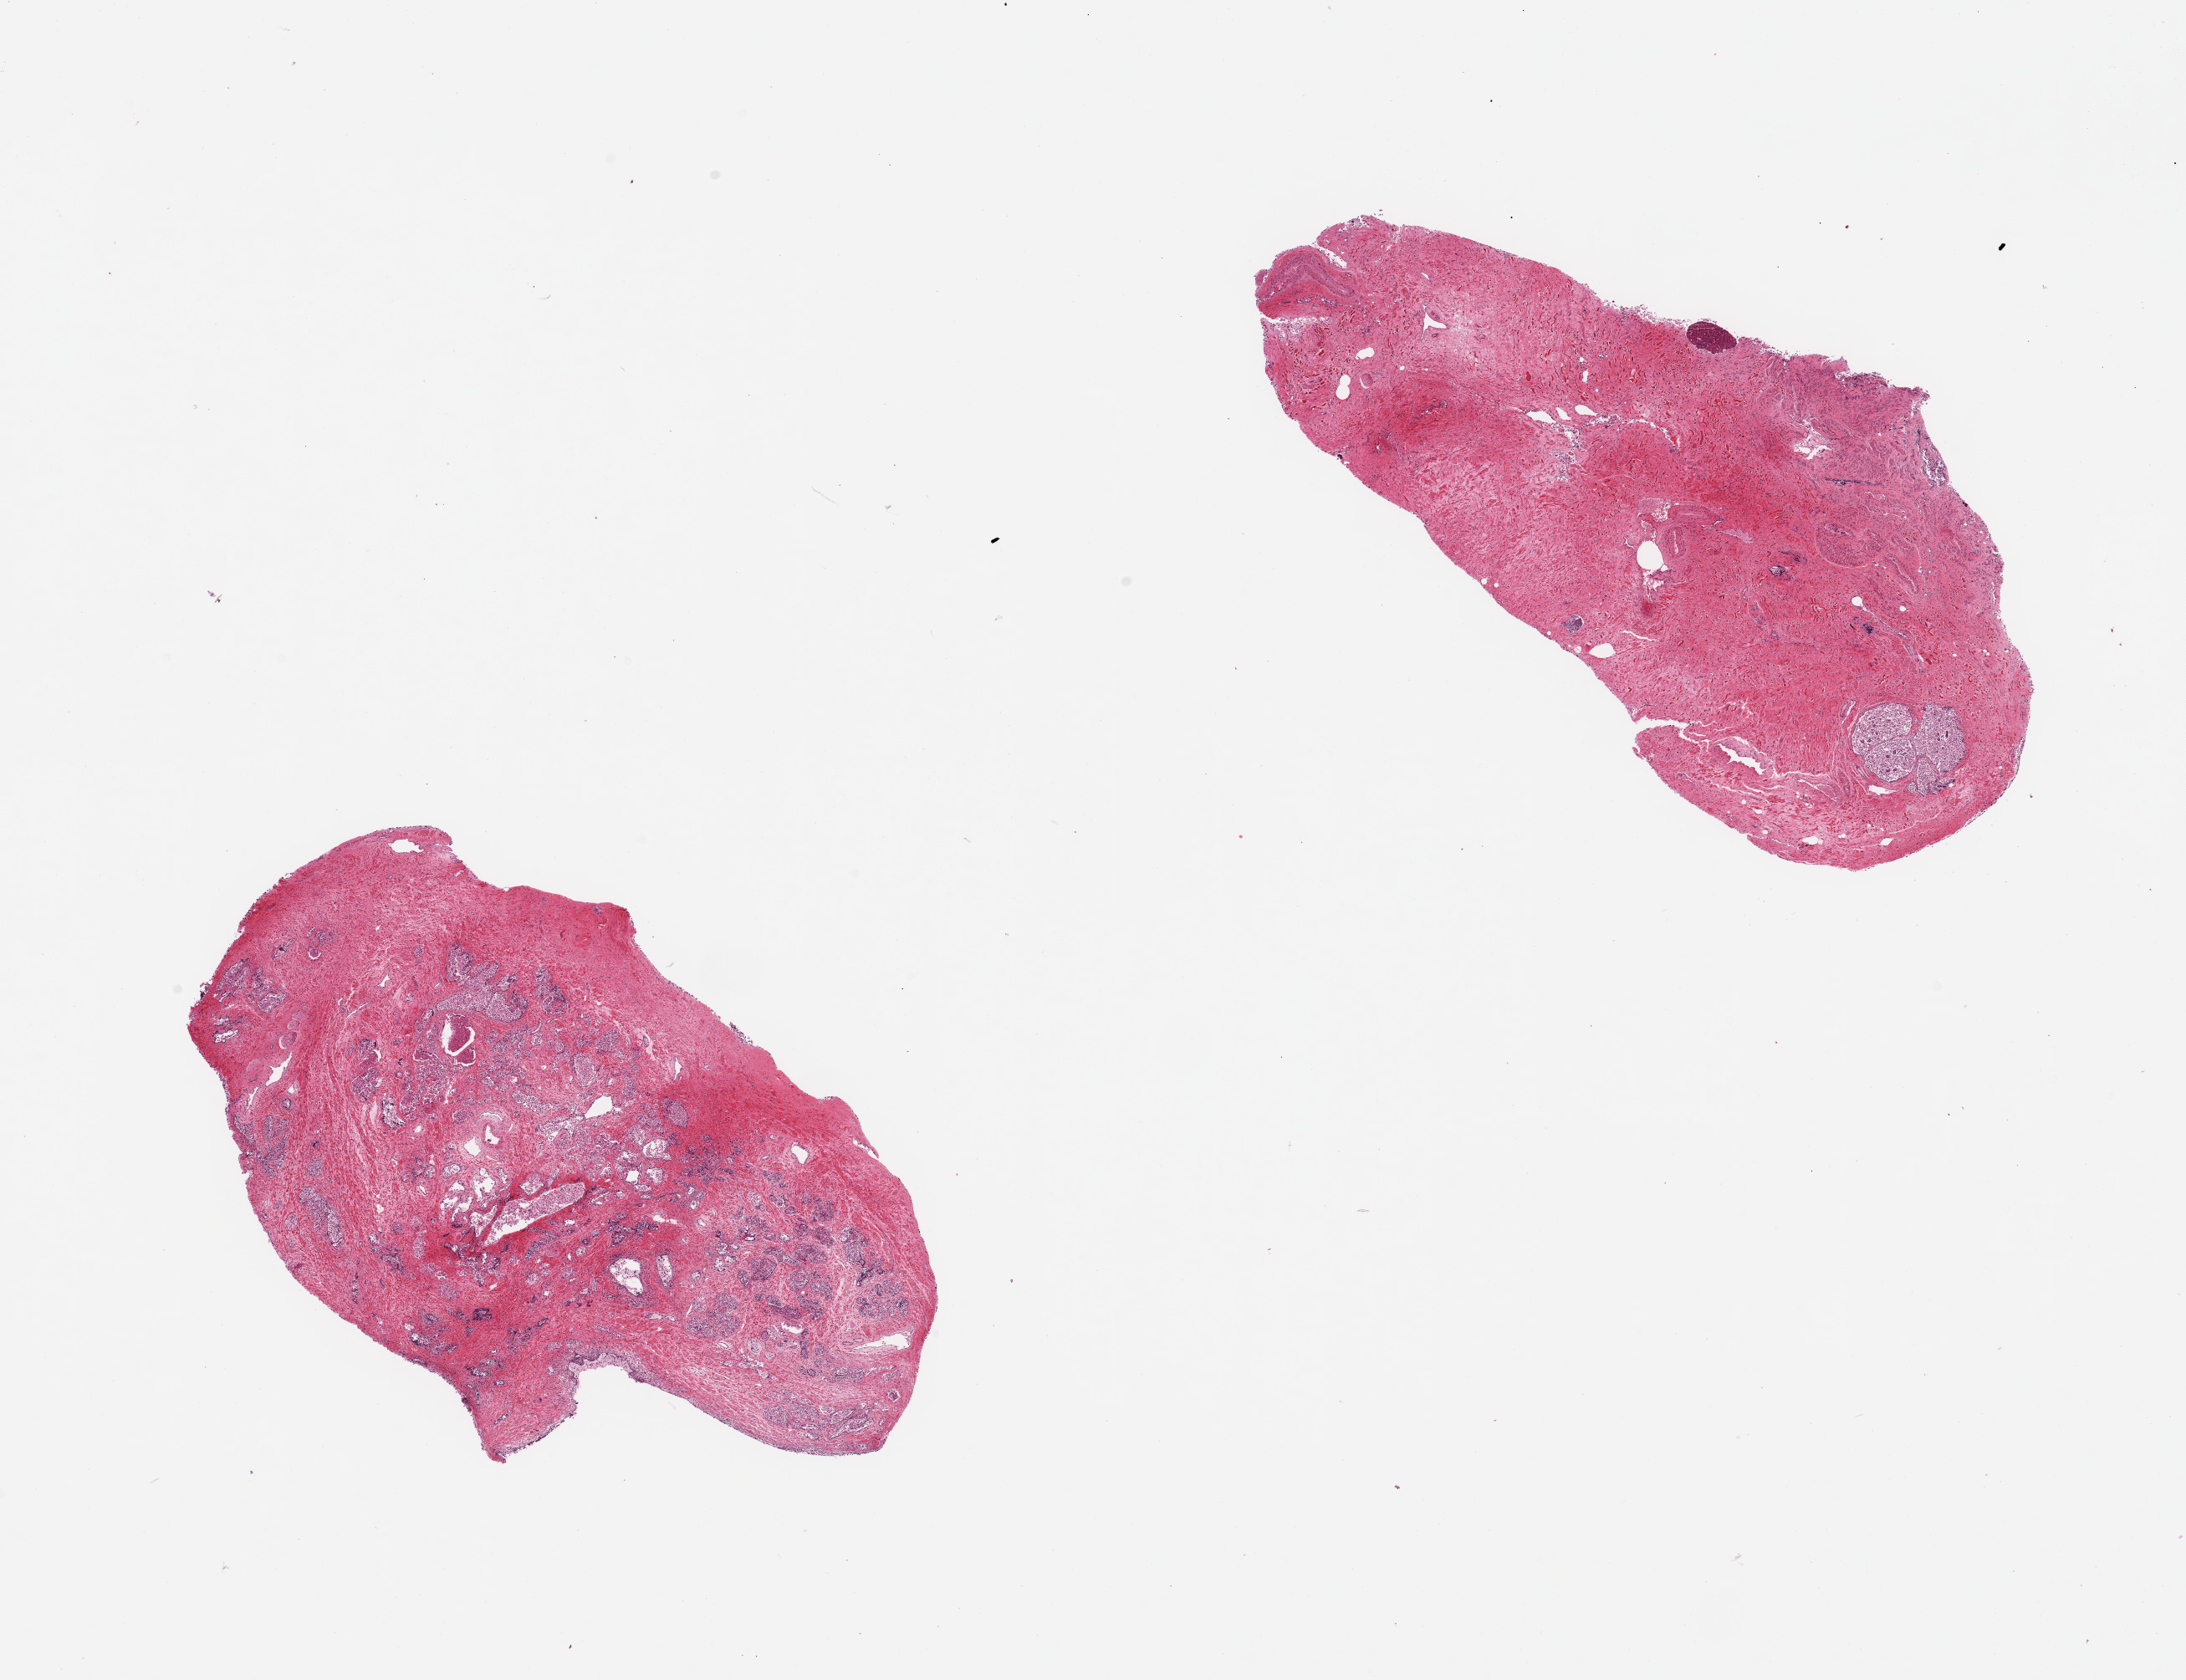
Digitized haematoxylin and eosin-stained section — shown as a low-resolution overview of the whole scanned area (about 20.7 x 15.9 mm, acquisition: 20x scan); PAXgene-fixed paraffin-embedded (PFPE) section; sampled site (target tissue): prostate; donor tissue sample. Male donor.
* review note (as recorded): 2 pieces; glands autolyzed, stroma intact; 1 piece is largely stroma with a 0.47 mm piece of carried over liver on edge